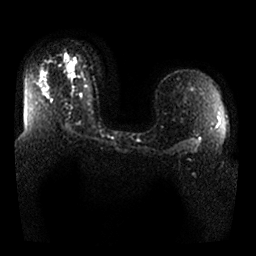
Breast MRI, one axial slice. Position 18 of 25 along the scan axis. Diffusion-weighted series; image 2 of 4 stored at this slice position (different b-values; order by instance number). 1.5 T. 256 × 256 image matrix, field of view 360 × 360 mm. Female patient.
Annotated regions visible in this slice (manually delineated by an expert):
- tumour on diffusion-weighted imaging: bounding box (x1, y1, x2, y2) in pixels: (69, 61, 75, 78)